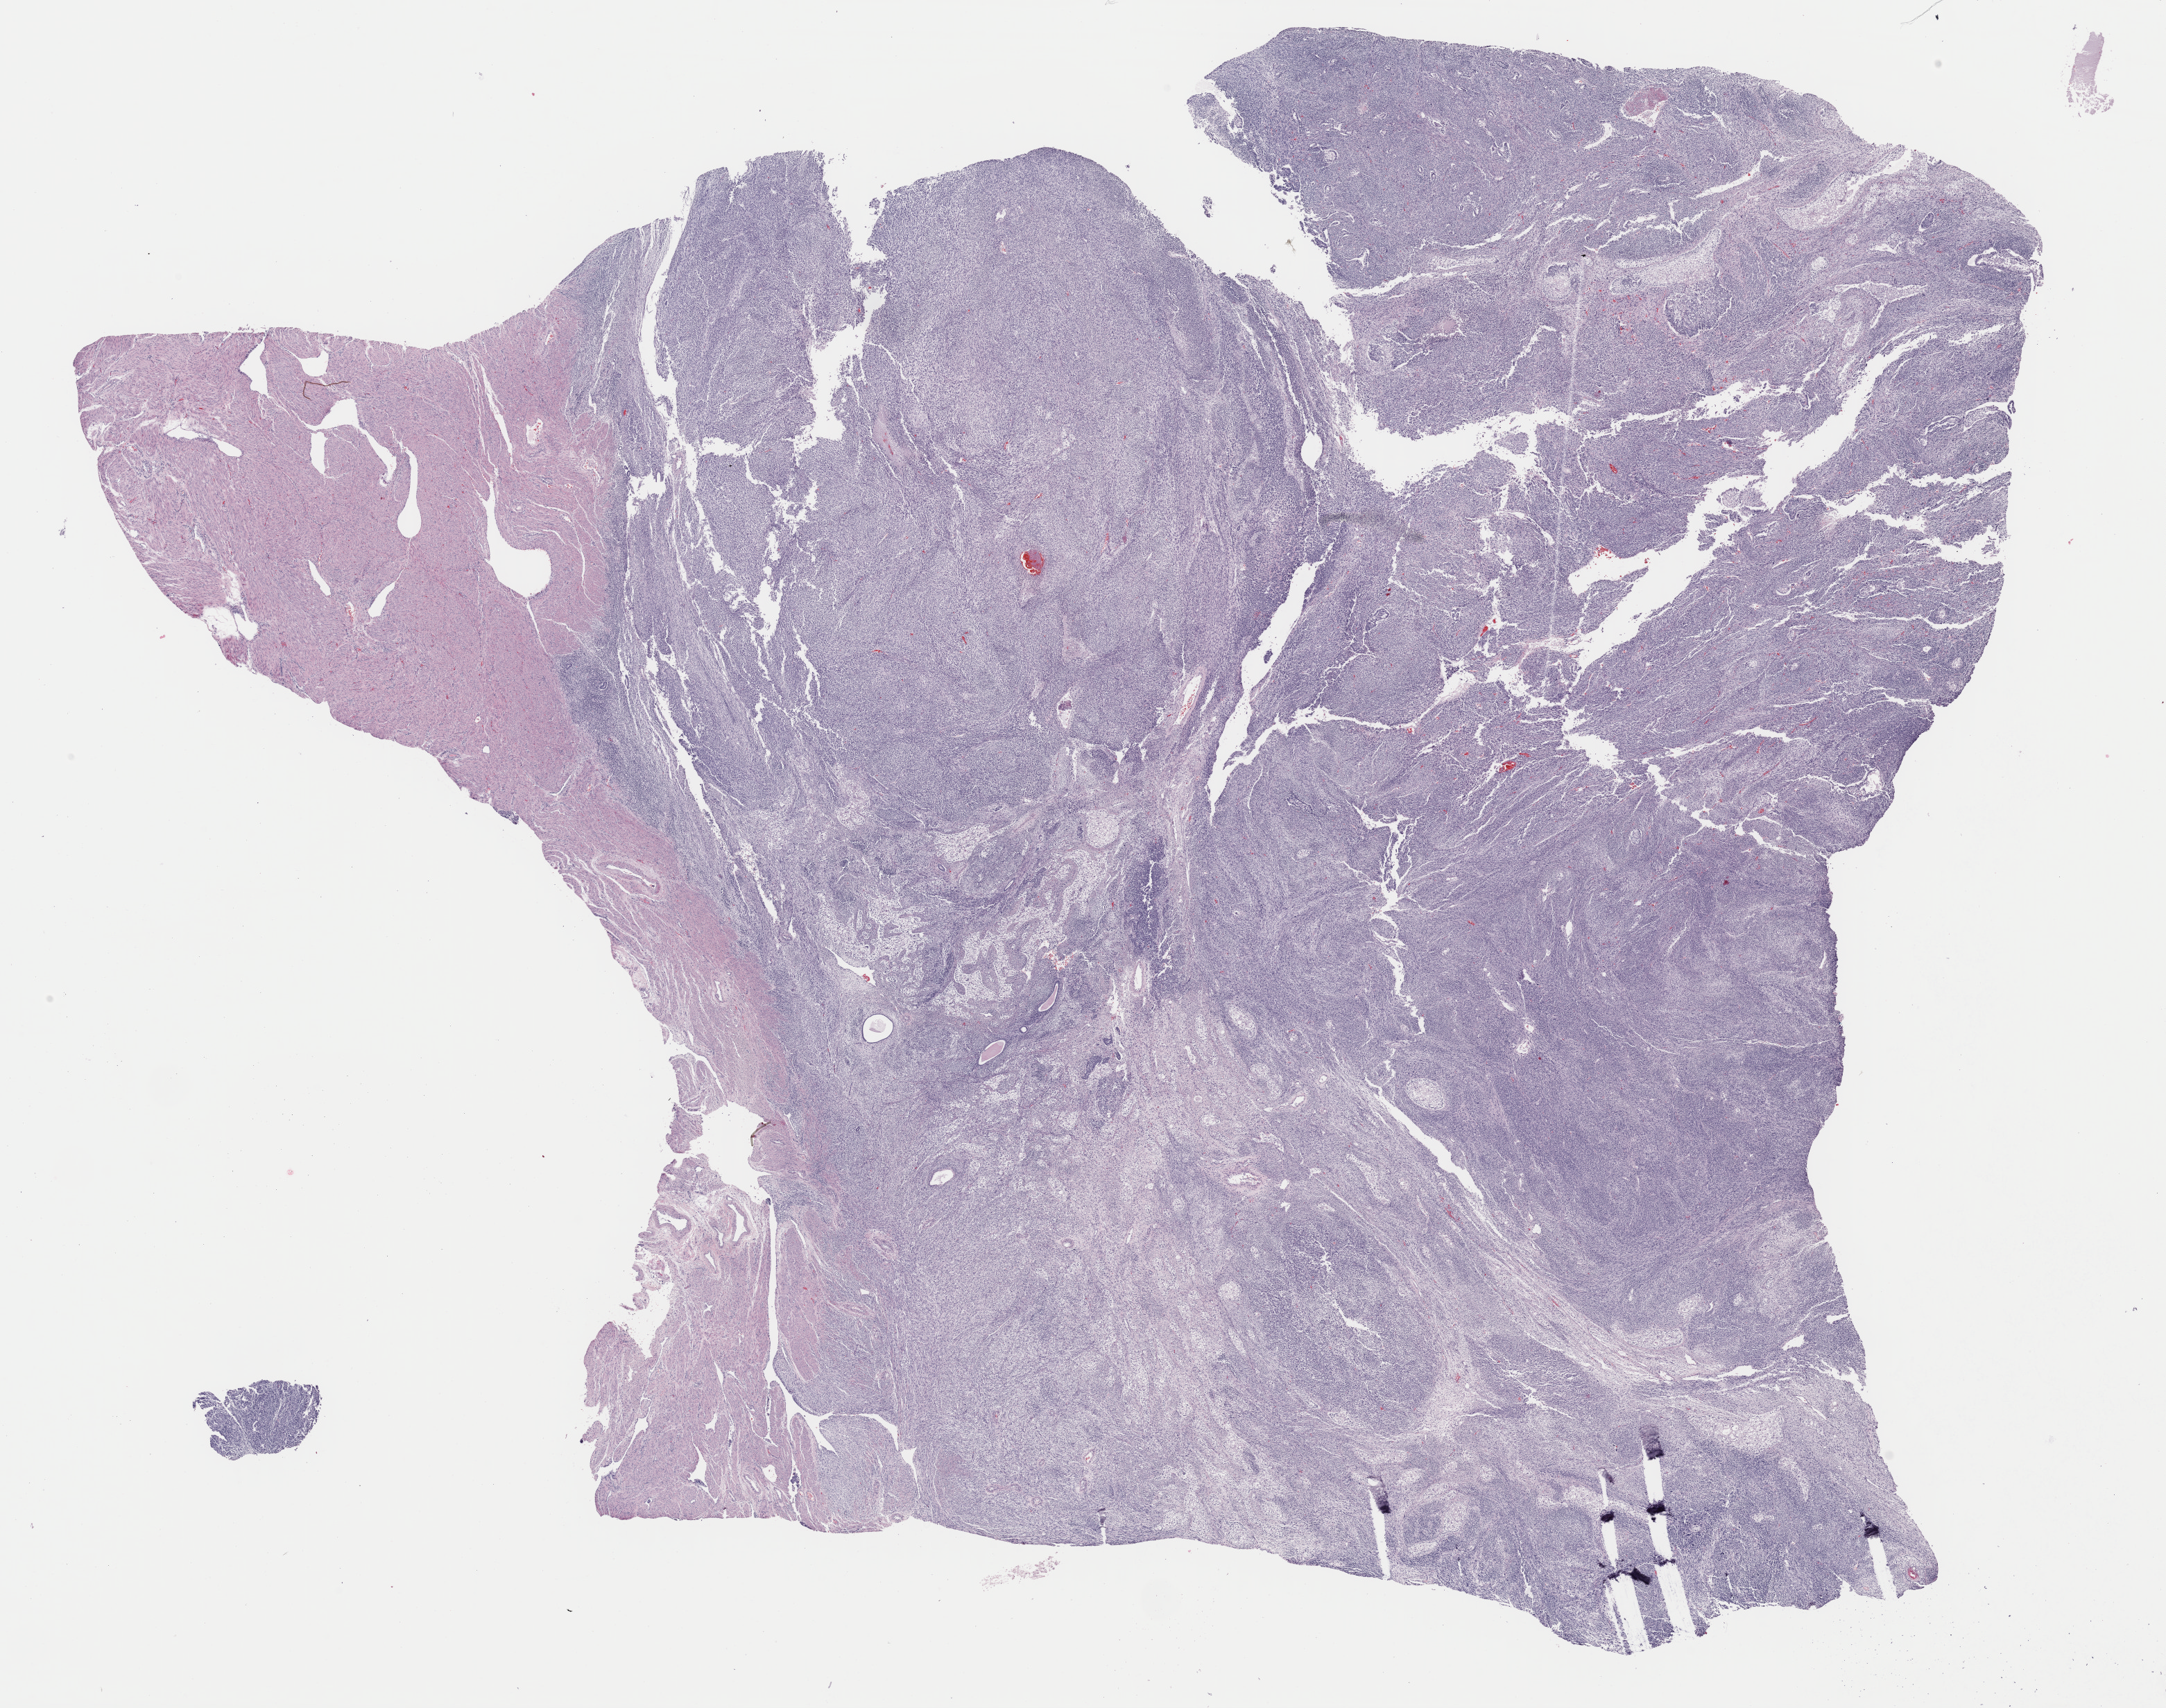
H&E whole-slide image, a low-resolution overview of the entire scanned area, about 24.7 x 19.5 mm; formalin-fixed paraffin-embedded (FFPE) diagnostic section; uterus, primary tumour sample. Patient: female, age at initial diagnosis 62 years.
- diagnosis: Mullerian mixed tumor (myometrium)
- FIGO stage: IVB